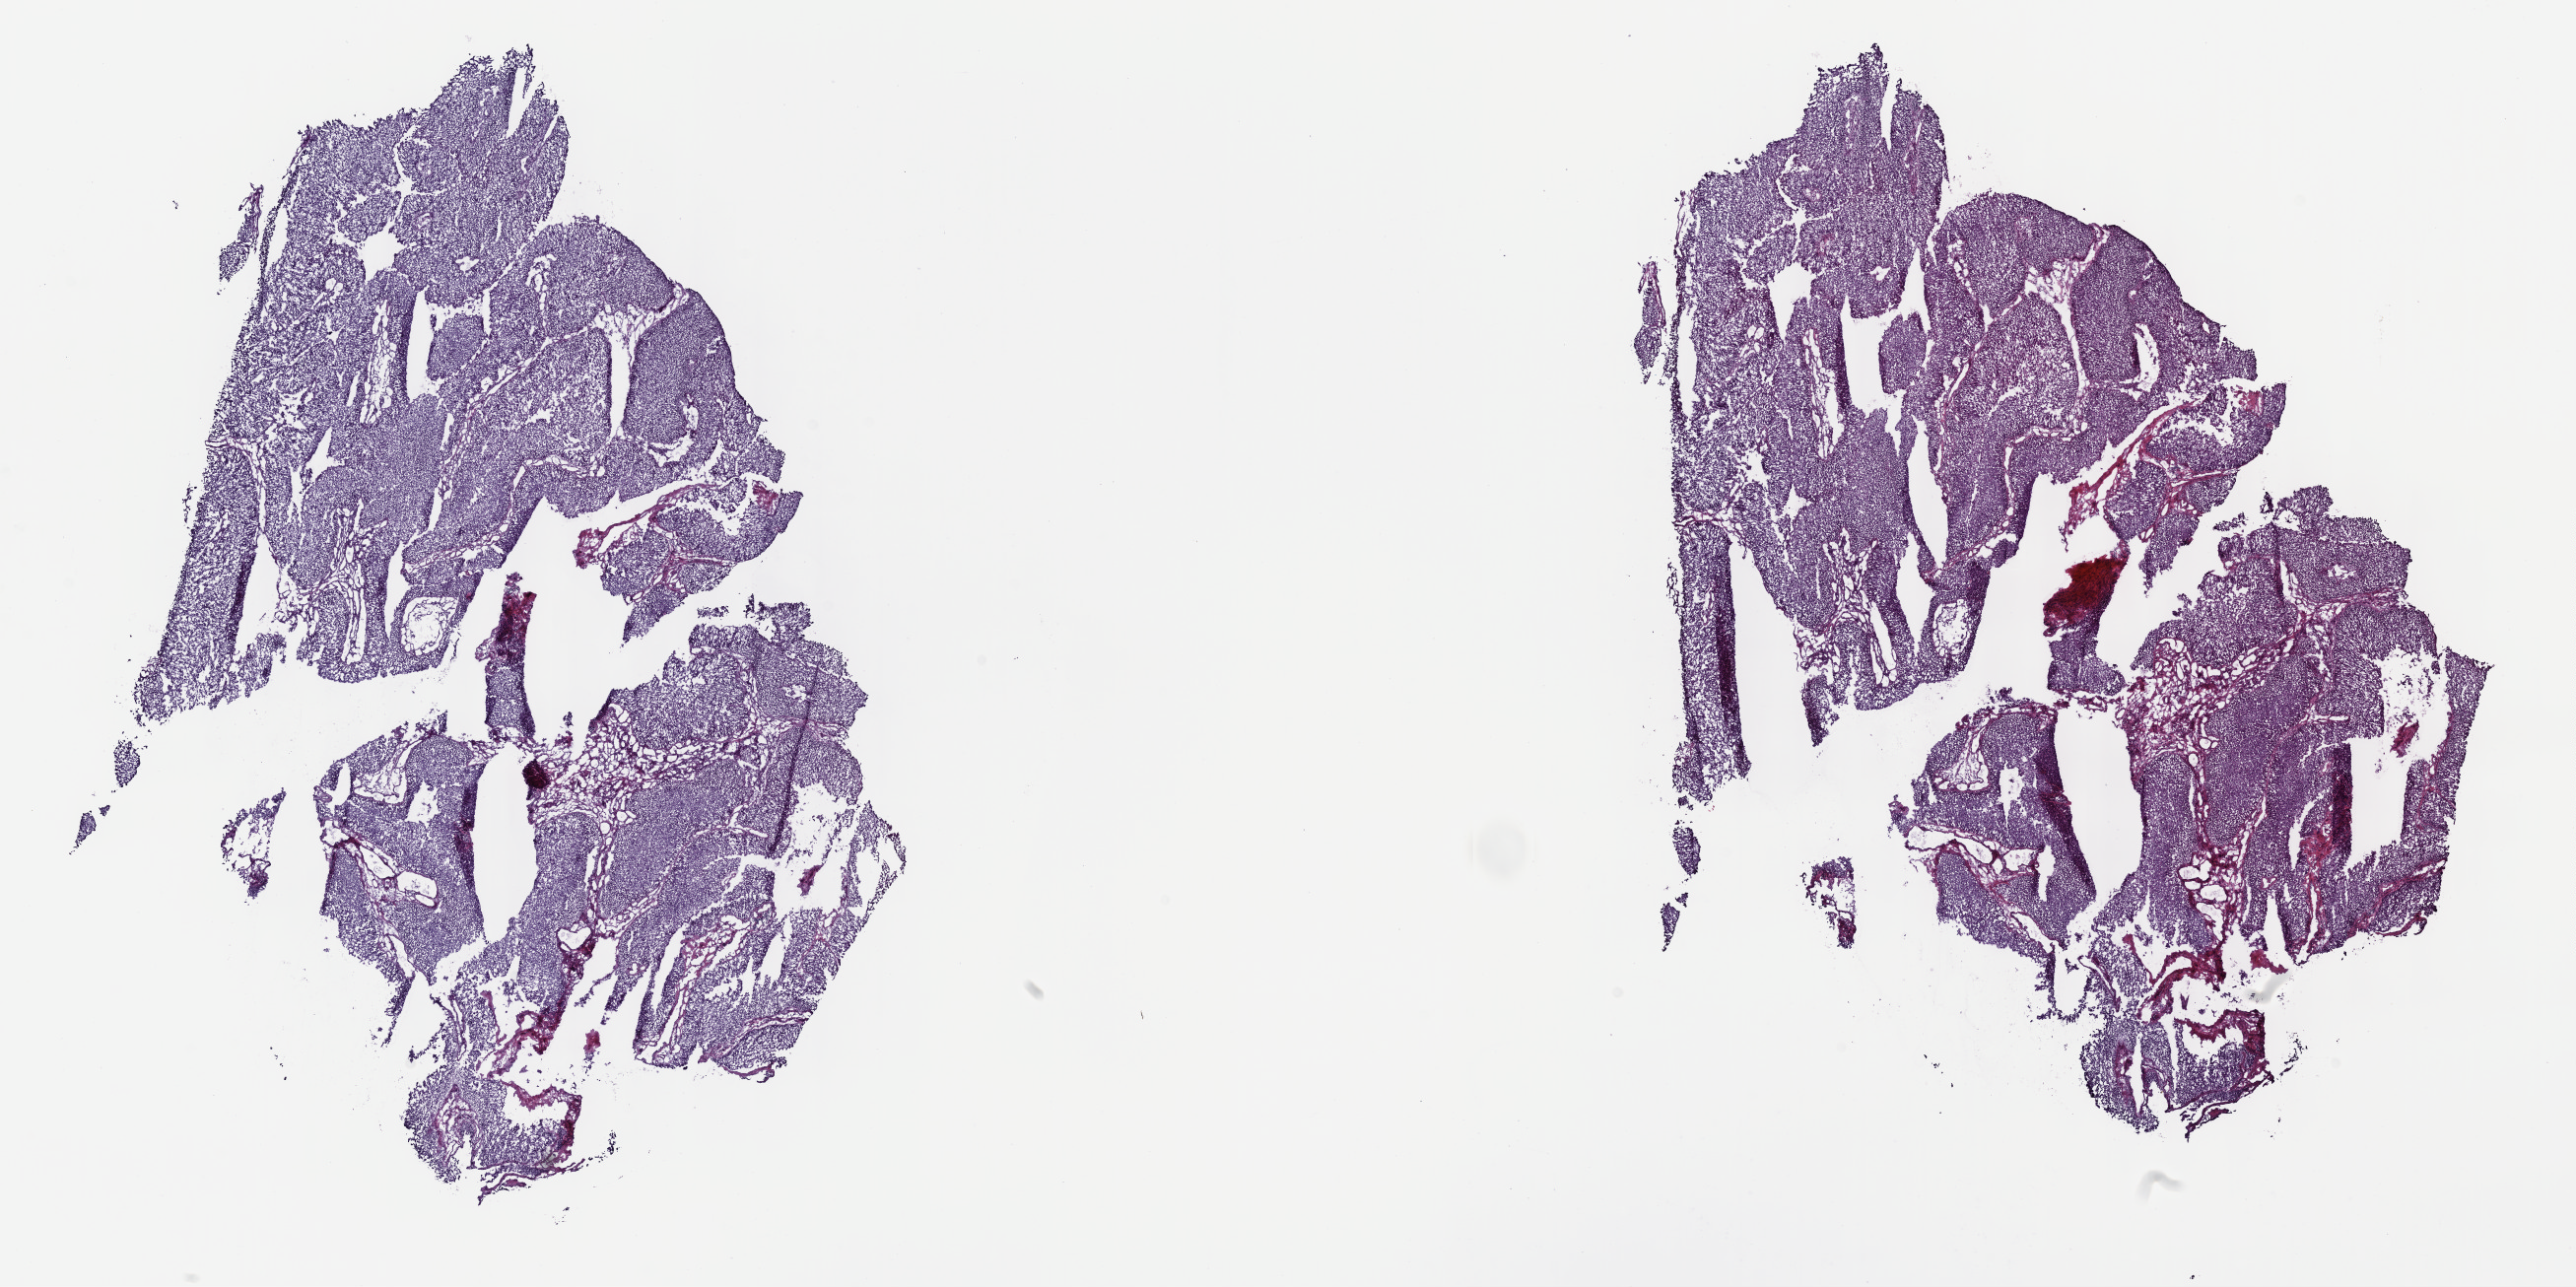
Digitized H&E-stained tissue section (whole slide), low-resolution overview of the scanned area, about 21.1 x 10.6 mm. Frozen section from the top of the tissue portion. Primary tumour sample from the bladder. Male patient; age at initial diagnosis 60 years. Pathologist review of this section (percent, as recorded): tumour cells 100%, tumour nuclei 80%.
Histologic diagnosis: Papillary transitional cell carcinoma (lateral wall of bladder).